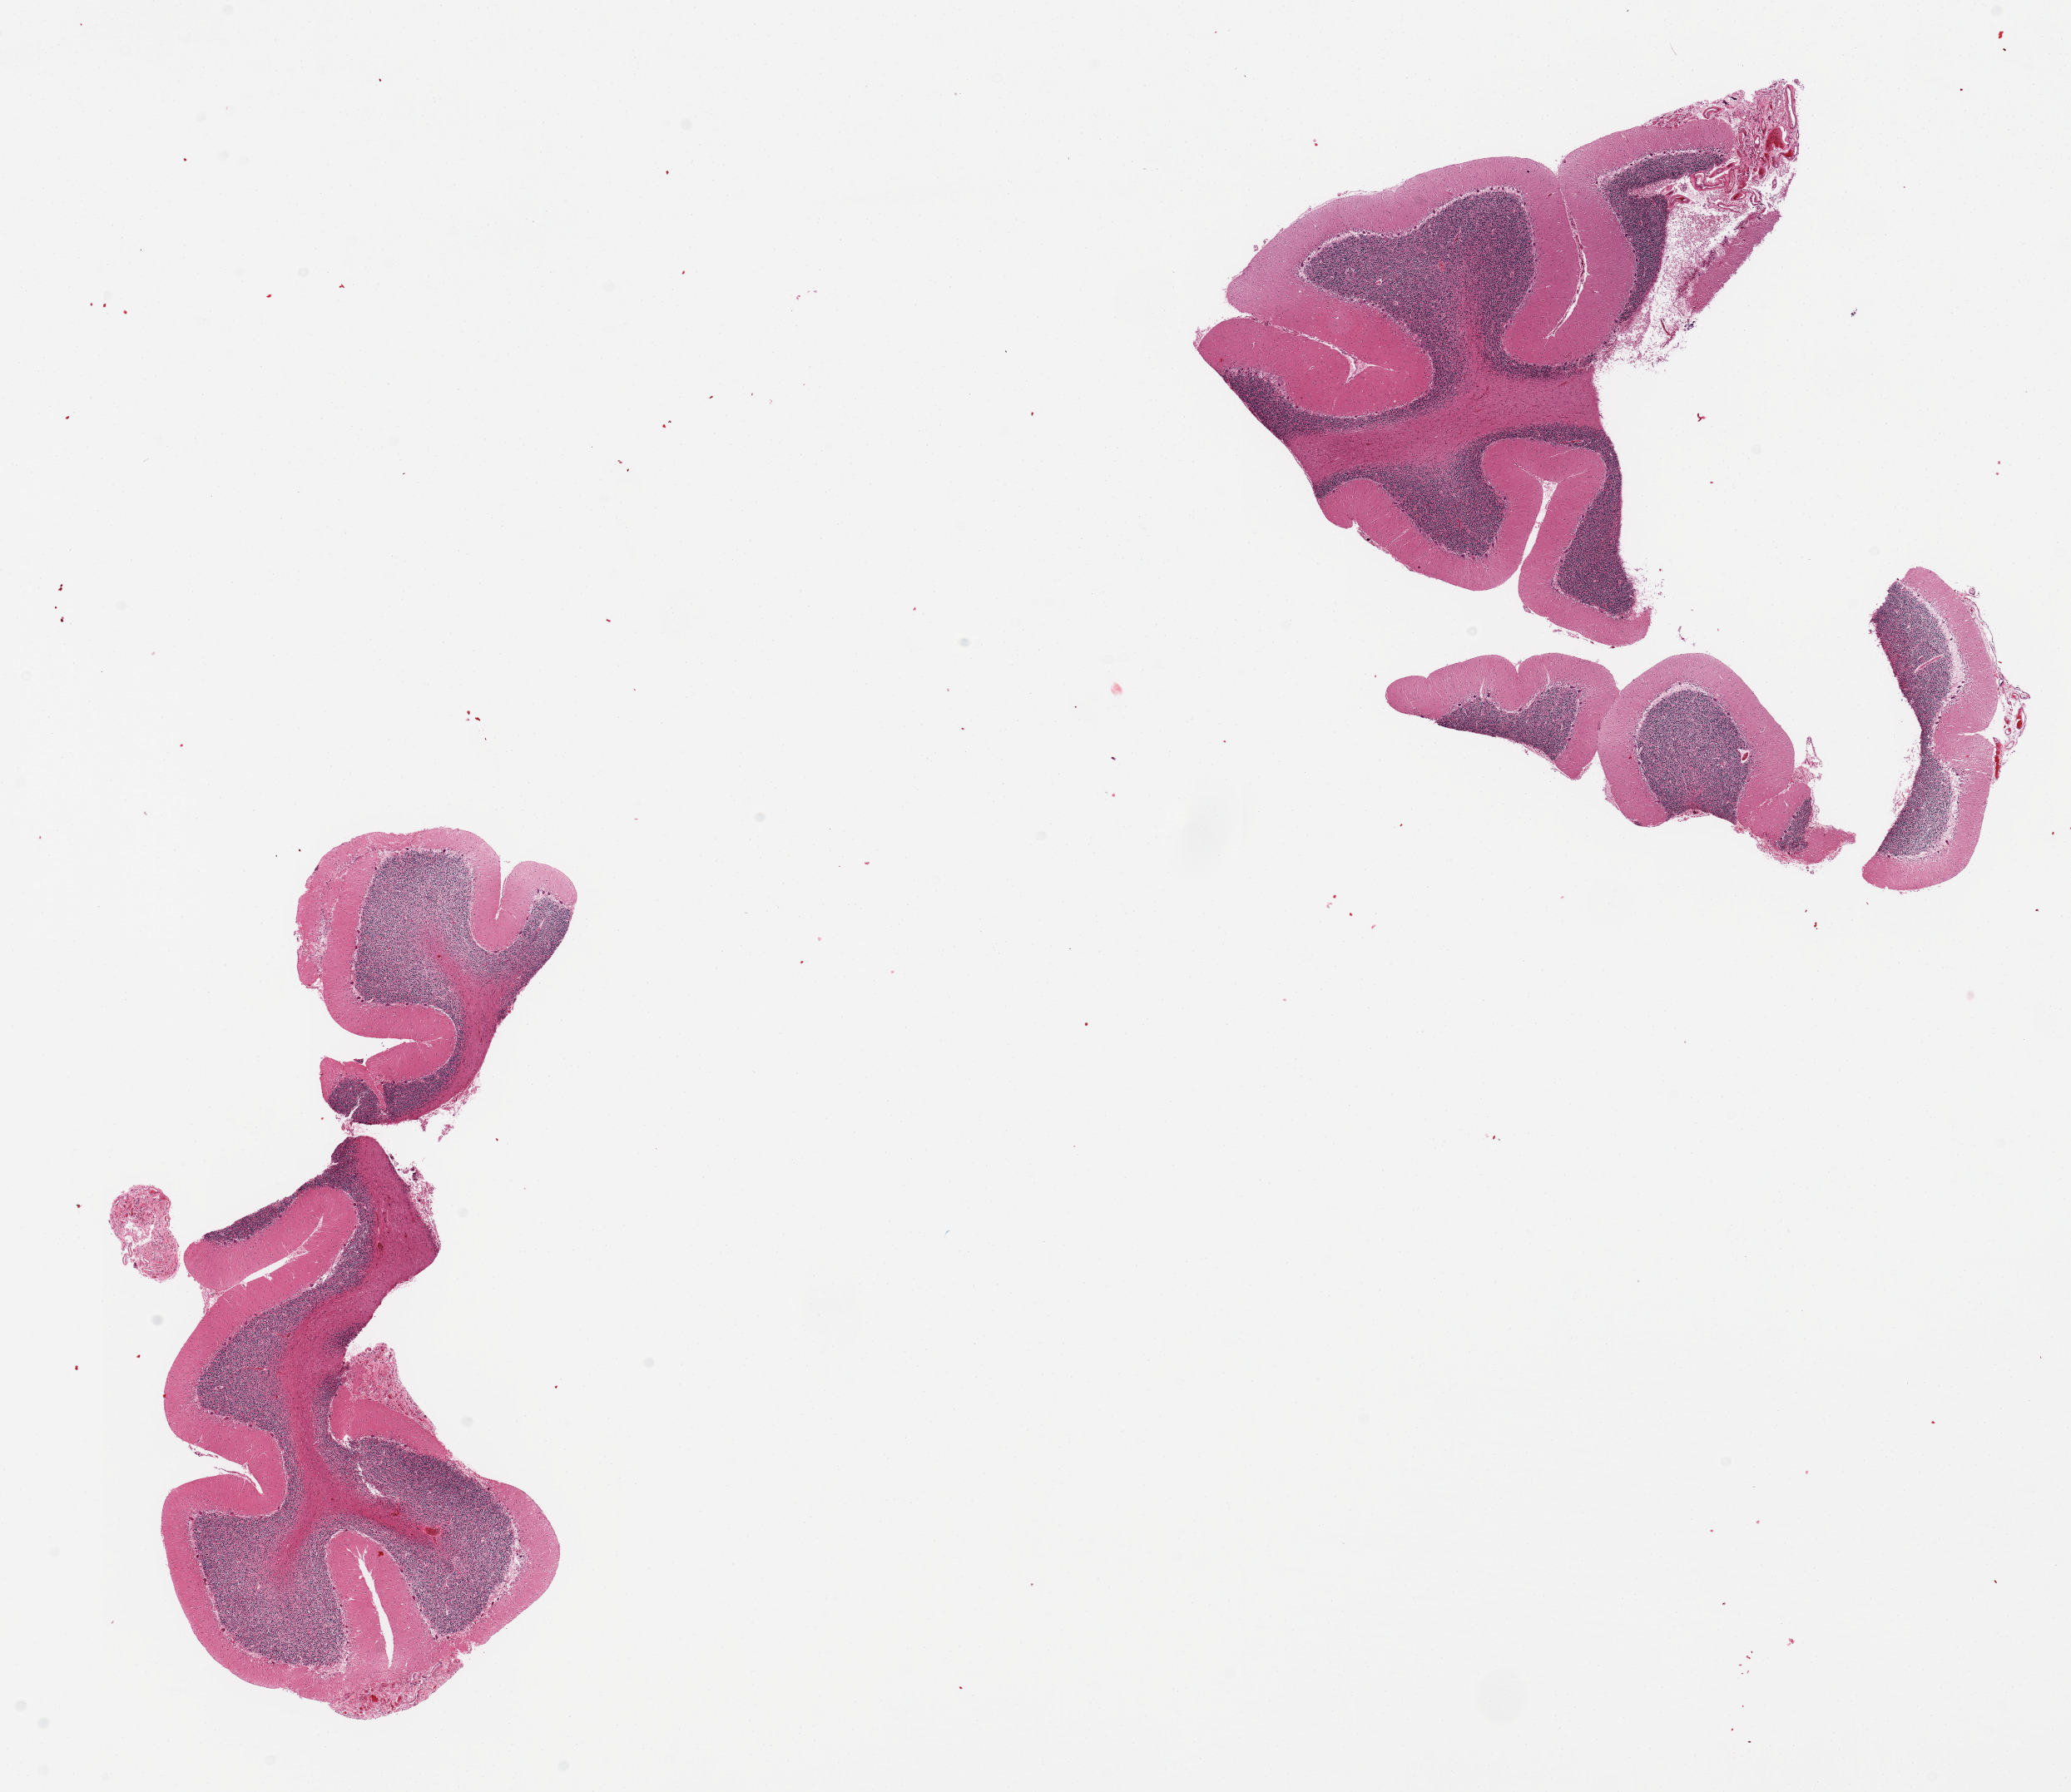
Whole-slide image, H&E stain, whole scanned area (about 19.7 x 17.0 mm, from a 20x scan) shown as a low-resolution overview; PAXgene-fixed paraffin-embedded (PFPE) section; target tissue: cerebellum; donor tissue sample. Donor sex: male.
Reviewer comment on this tissue sample: 2 pieces, Purkinje cells with some evidence of hypoxic damage.